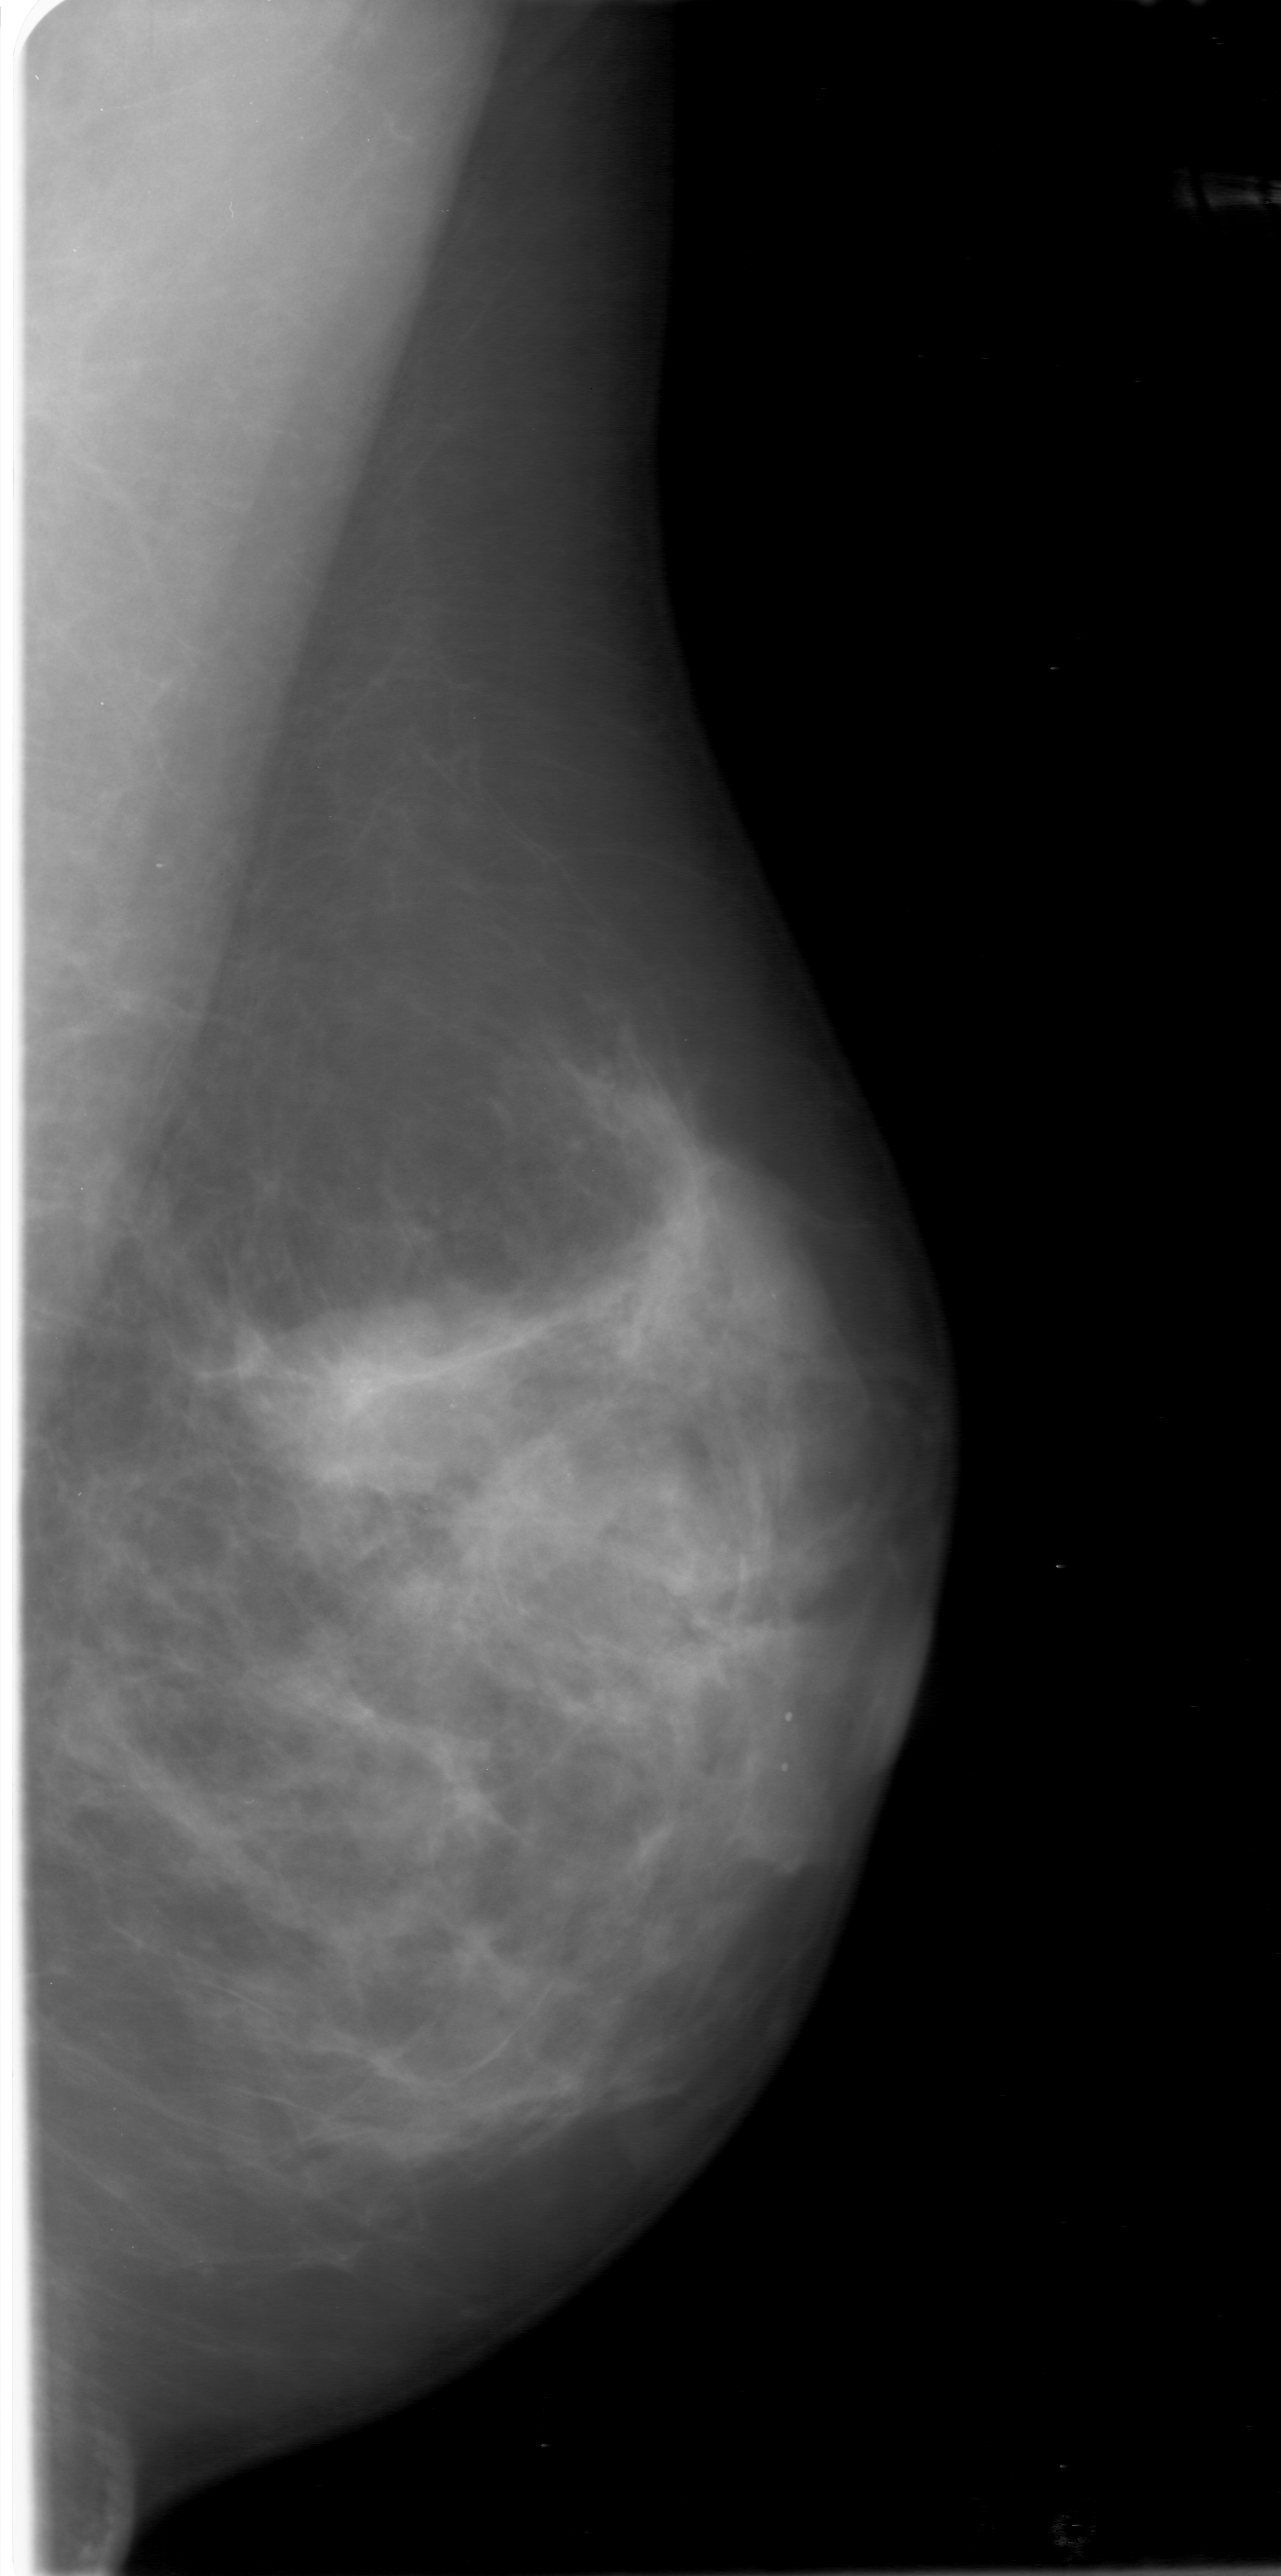
Mammogram (digitized film); left breast; MLO view.
- Radiologist-marked abnormalities on this image: calcifications, morphology amorphous, distribution segmental; BI-RADS assessment category 4; subtlety rating 3 on a 1 (subtle) to 5 (obvious) scale; pathology result (as recorded, not read from the image): malignant.